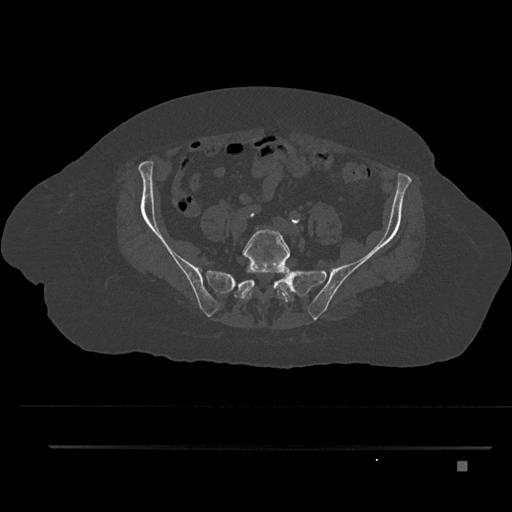
CT including the spine, one axial slice. Slice 22 of 797 in the series (ordered by position). 120 kVp. Bone window (W 1800 / L 400 HU). 512 × 512 image matrix. Female patient, age 76 years. From the clinical record (not read from this slice): primary cancer: lung.
Annotated regions visible in this slice (semi-automatically segmented with operator editing):
- L5 vertebra: bounding box (x1, y1, x2, y2) in pixels: (241, 227, 290, 302)